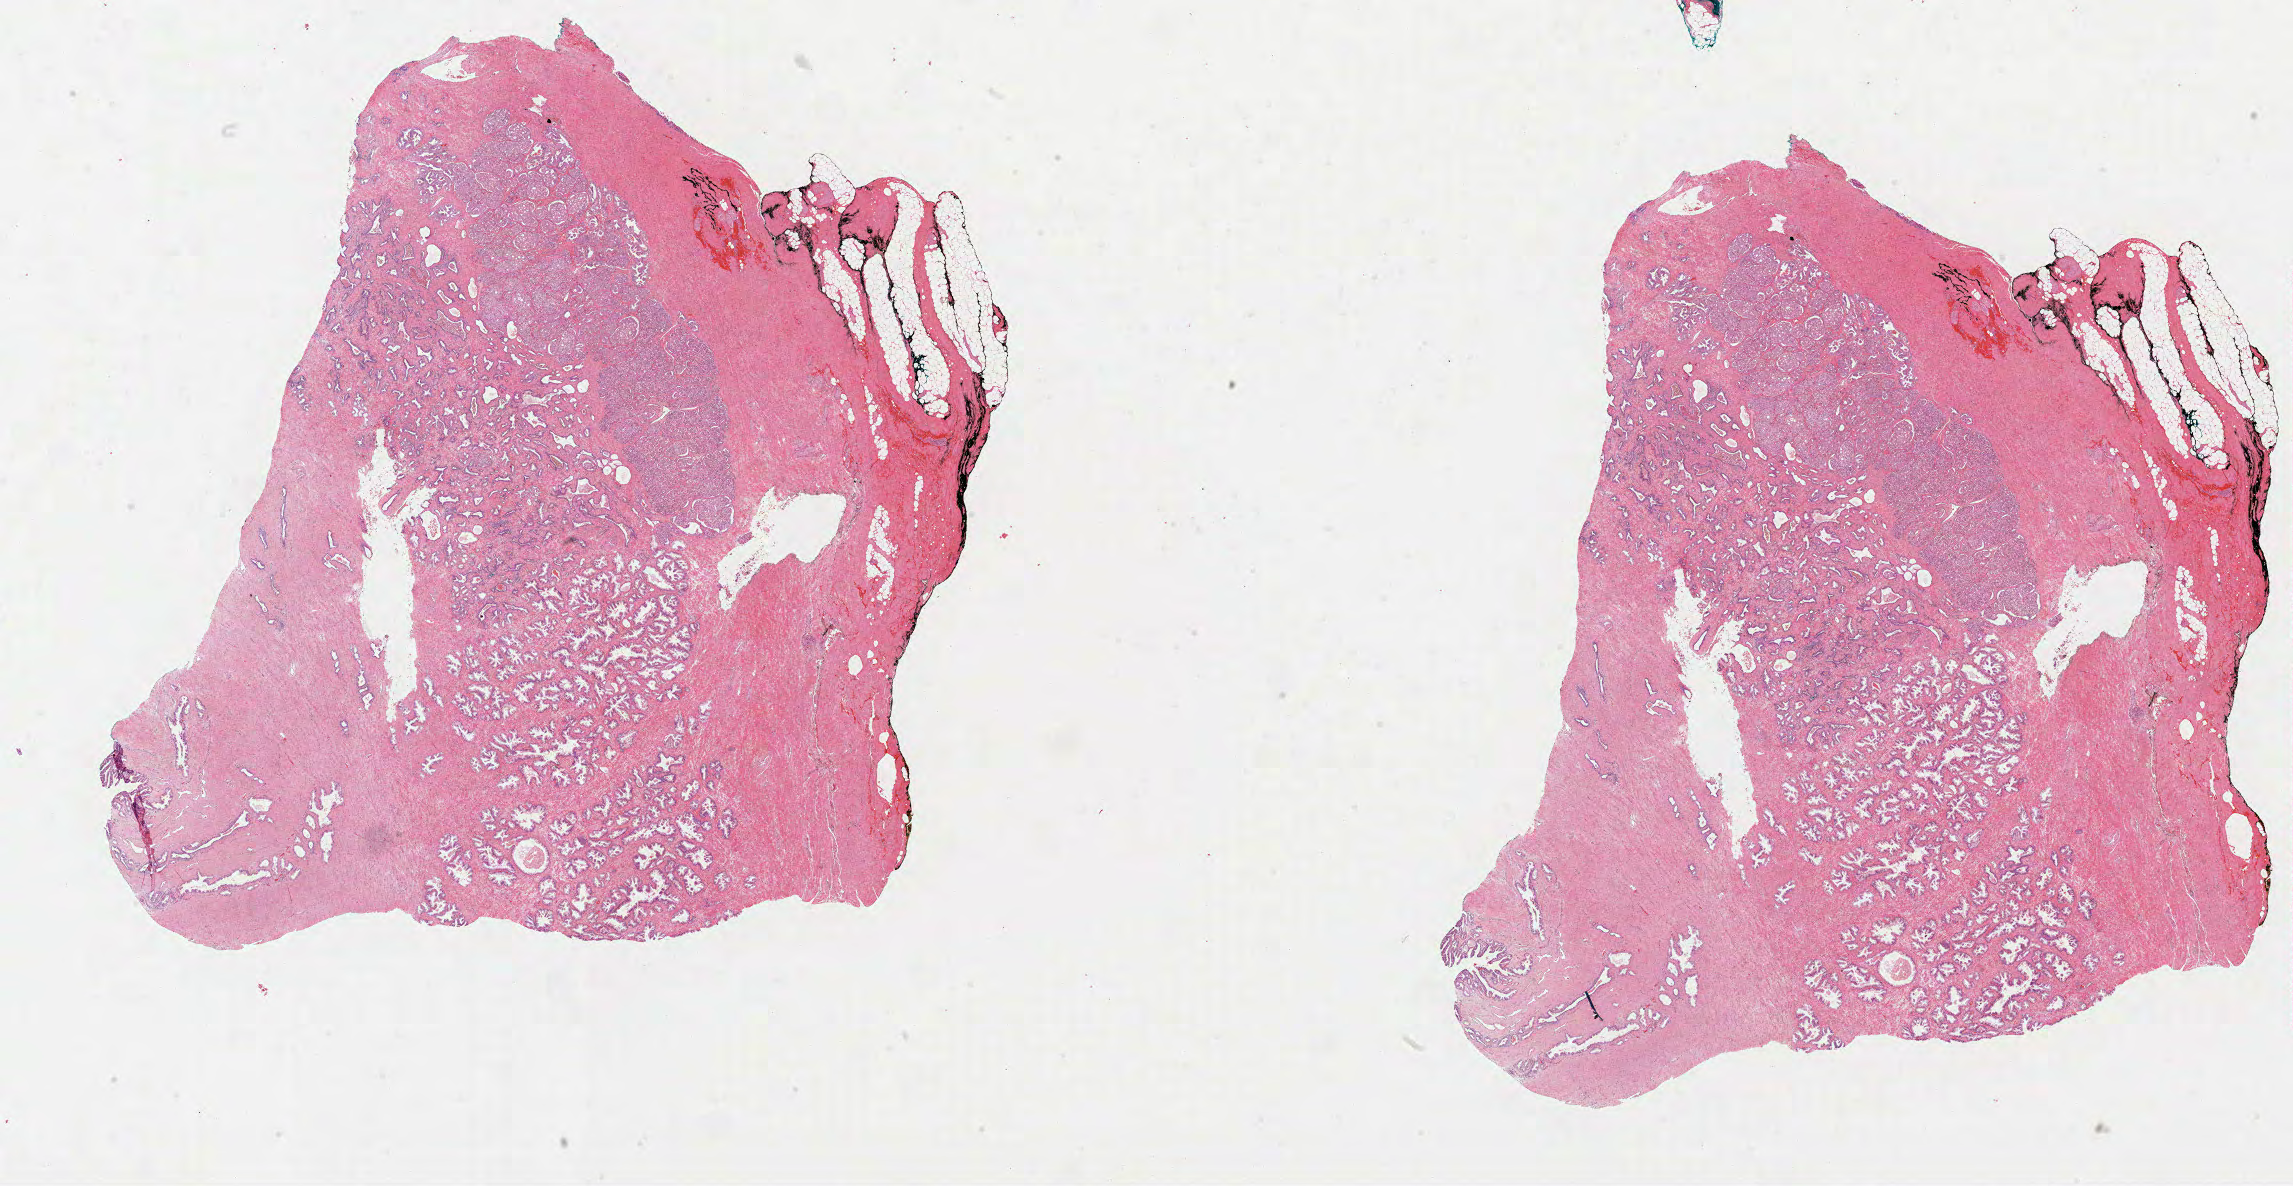
Digitized Hematoxylin and eosin (H&E) stained tissue section (whole slide), whole scanned area (about 37.0 x 19.1 mm) shown as a low-resolution overview; formalin-fixed paraffin-embedded (FFPE) diagnostic section; sample: primary tumour, prostate. Male, age 55 years at initial diagnosis. Gleason score: 7 (4+3).
Laterality: bilateral. Histologic diagnosis: Acinar cell carcinoma (prostate gland).